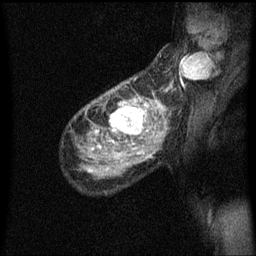
Breast MRI (dynamic contrast-enhanced), one sagittal slice; position 41 of 60 along the scan axis; dynamic contrast-enhanced series, image 2 of 3 at this slice position (ordered by acquisition); 1.5 T; TE 4.2 ms, TR 8.4 ms; 2 mm slice thickness; 256 × 256 image matrix, field of view 200 × 200 mm. Patient: female, 49 years.
Structures marked on this image (semi-automatic segmentation, software-assisted and operator-edited):
- analysis volume of interest (the breast-tissue region the enhancement analysis was run in; not a lesion): bounding box [x1, y1, x2, y2] px = [103, 90, 157, 151]
- tumour enhancement mask (voxels above the 70 % enhancement threshold inside the analysis volume of interest): [110, 98, 157, 151]